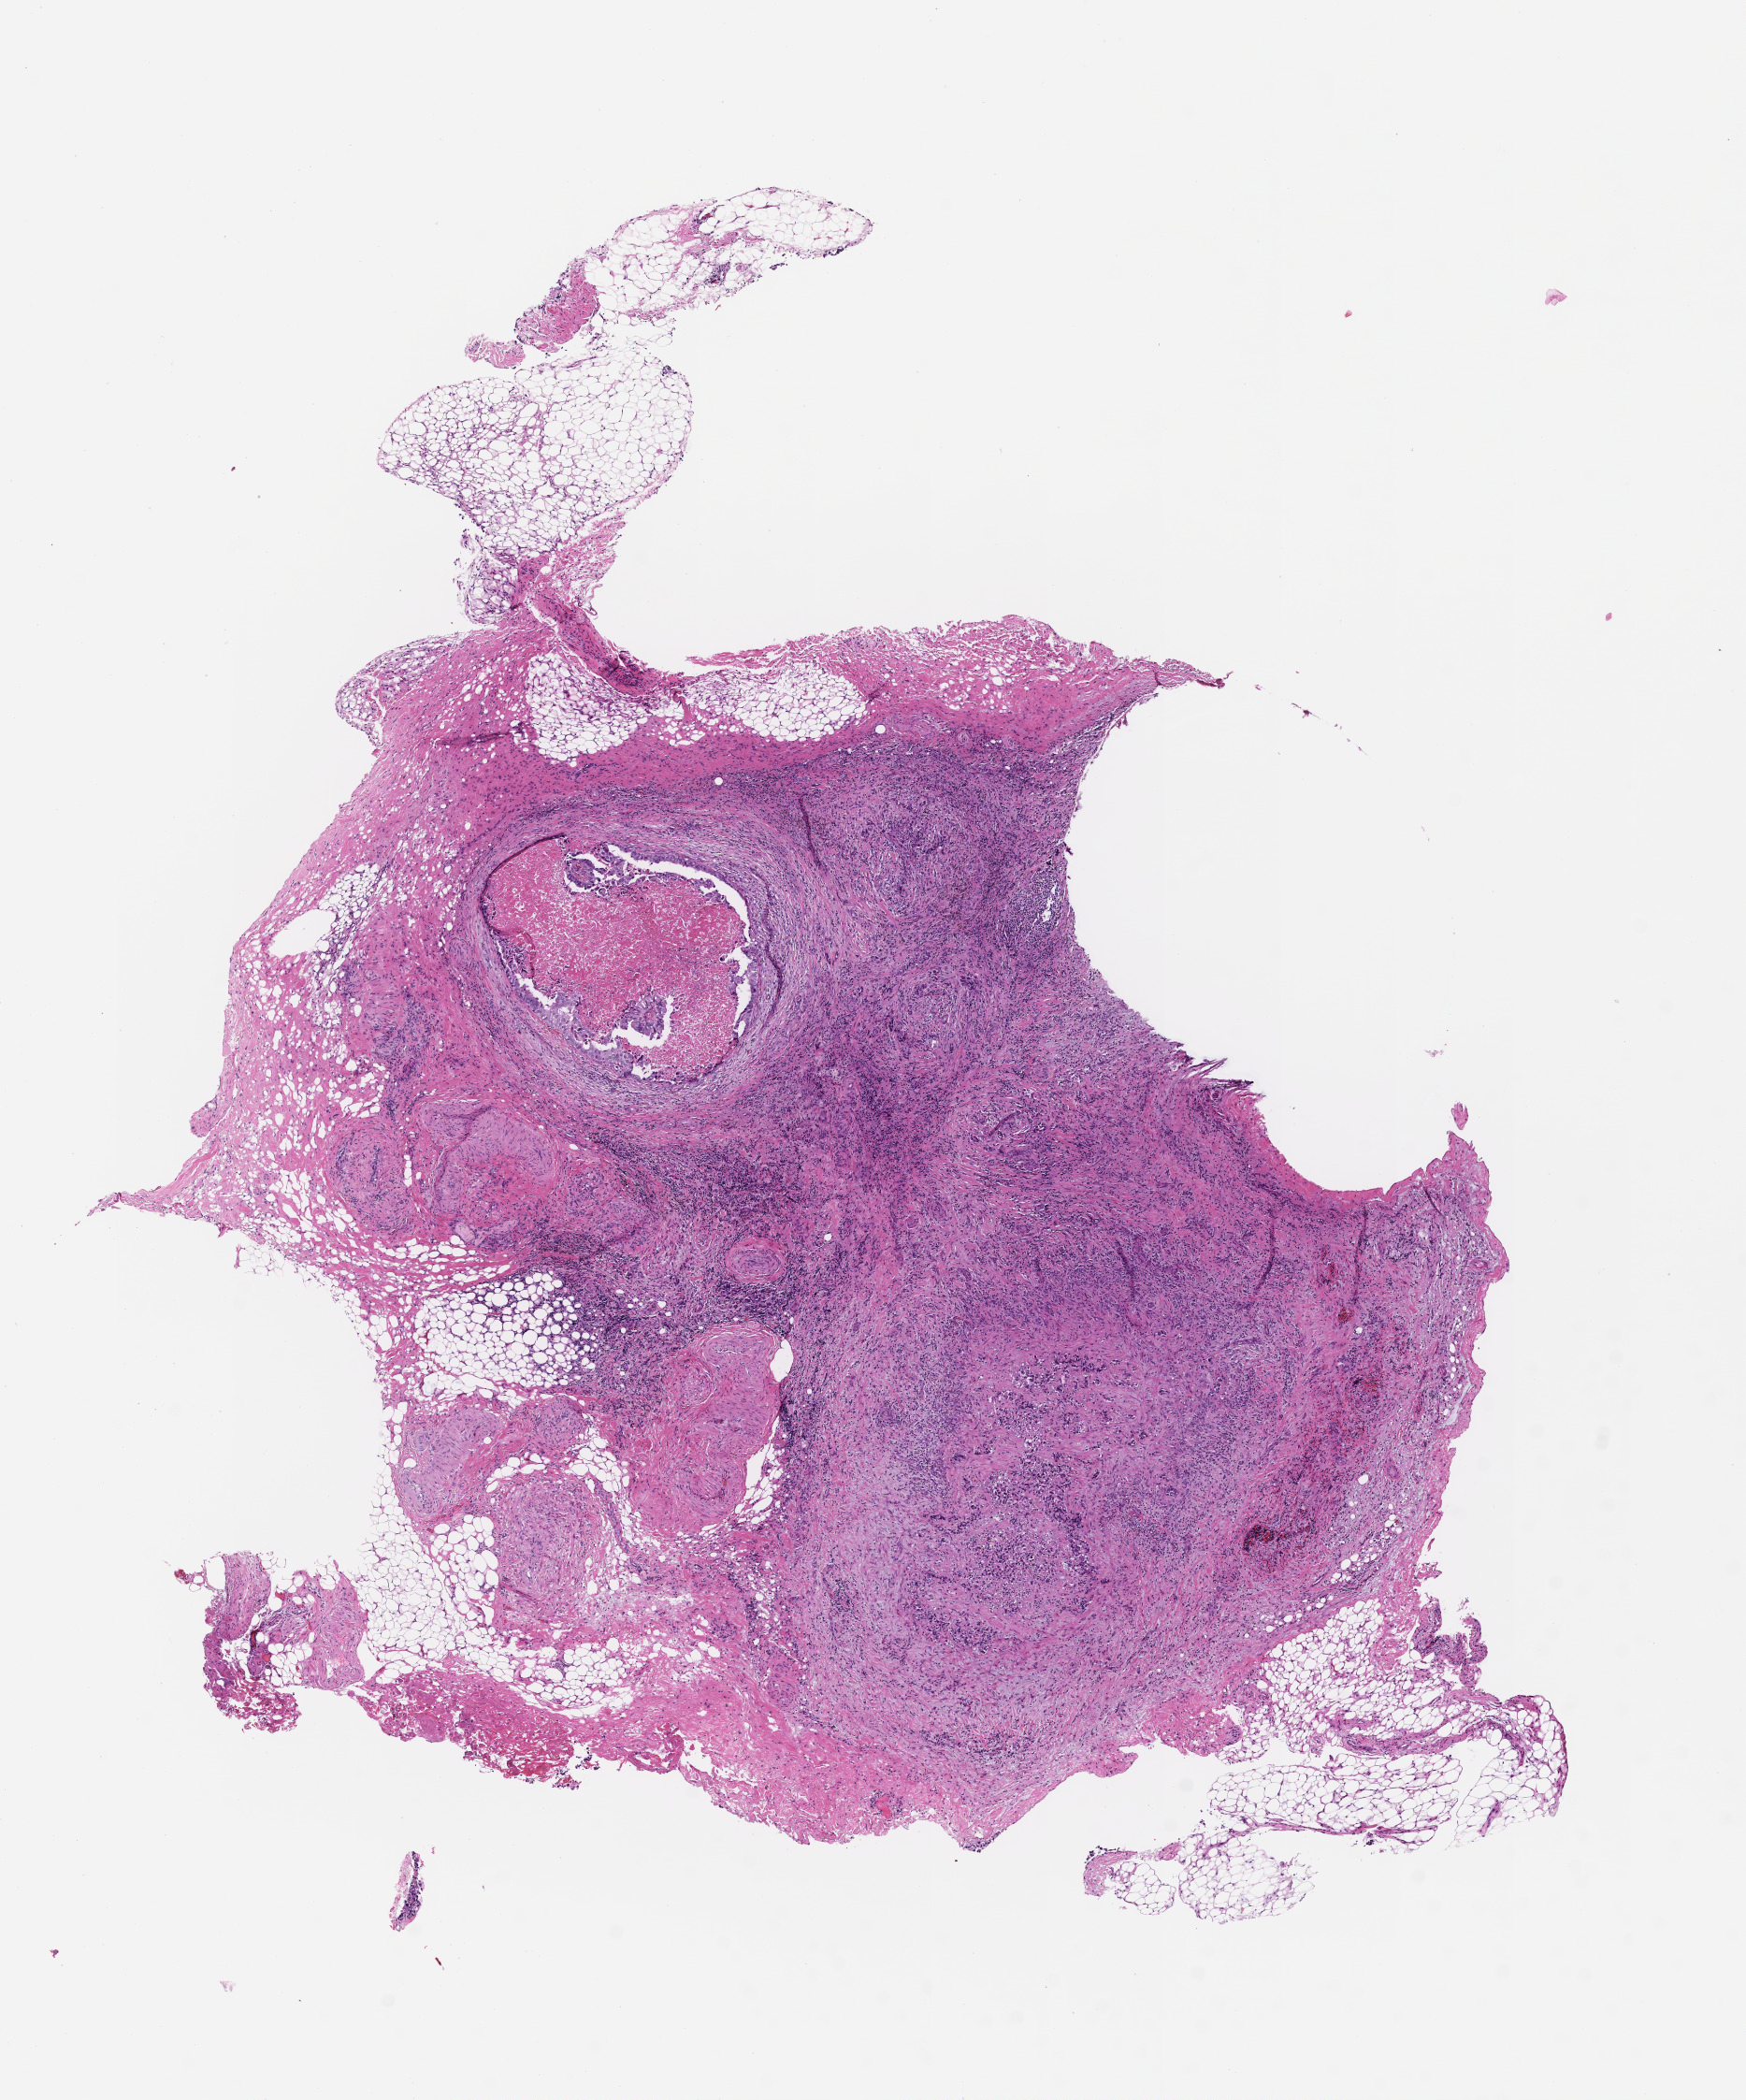
Whole-slide image, hematoxylin and eosin (H&E) stain — whole scanned area (about 7.5 x 9.1 mm) shown as a low-resolution overview, FFPE section, specimen time point: archival tissue. Patient sex: female.
* this section: metastasis (sampled organ not recorded)
* primary diagnosis of the patient: Non-Small Cell Lung Carcinoma